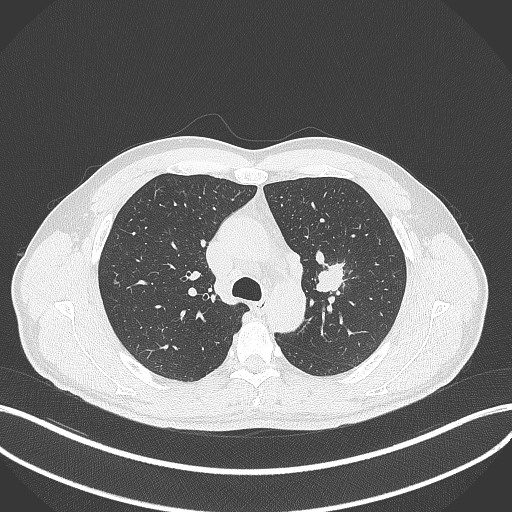
Chest CT, one axial slice; position 293 of 392 along the scan axis; reconstruction kernel B70f; lung window (W 1500 / L -600 HU); 1 mm slice thickness; 512 × 512 image matrix, field of view 400 × 400 mm. Male patient, age 50 years. From the clinical record (not read from this slice): clinical TNM (as recorded): T1c N1 M1b.
Outlined on this slice (rectangle marked by the reading radiologist):
- lung tumour (recorded histology: squamous cell carcinoma): bounding box [x1, y1, x2, y2] px = [312, 258, 346, 295]